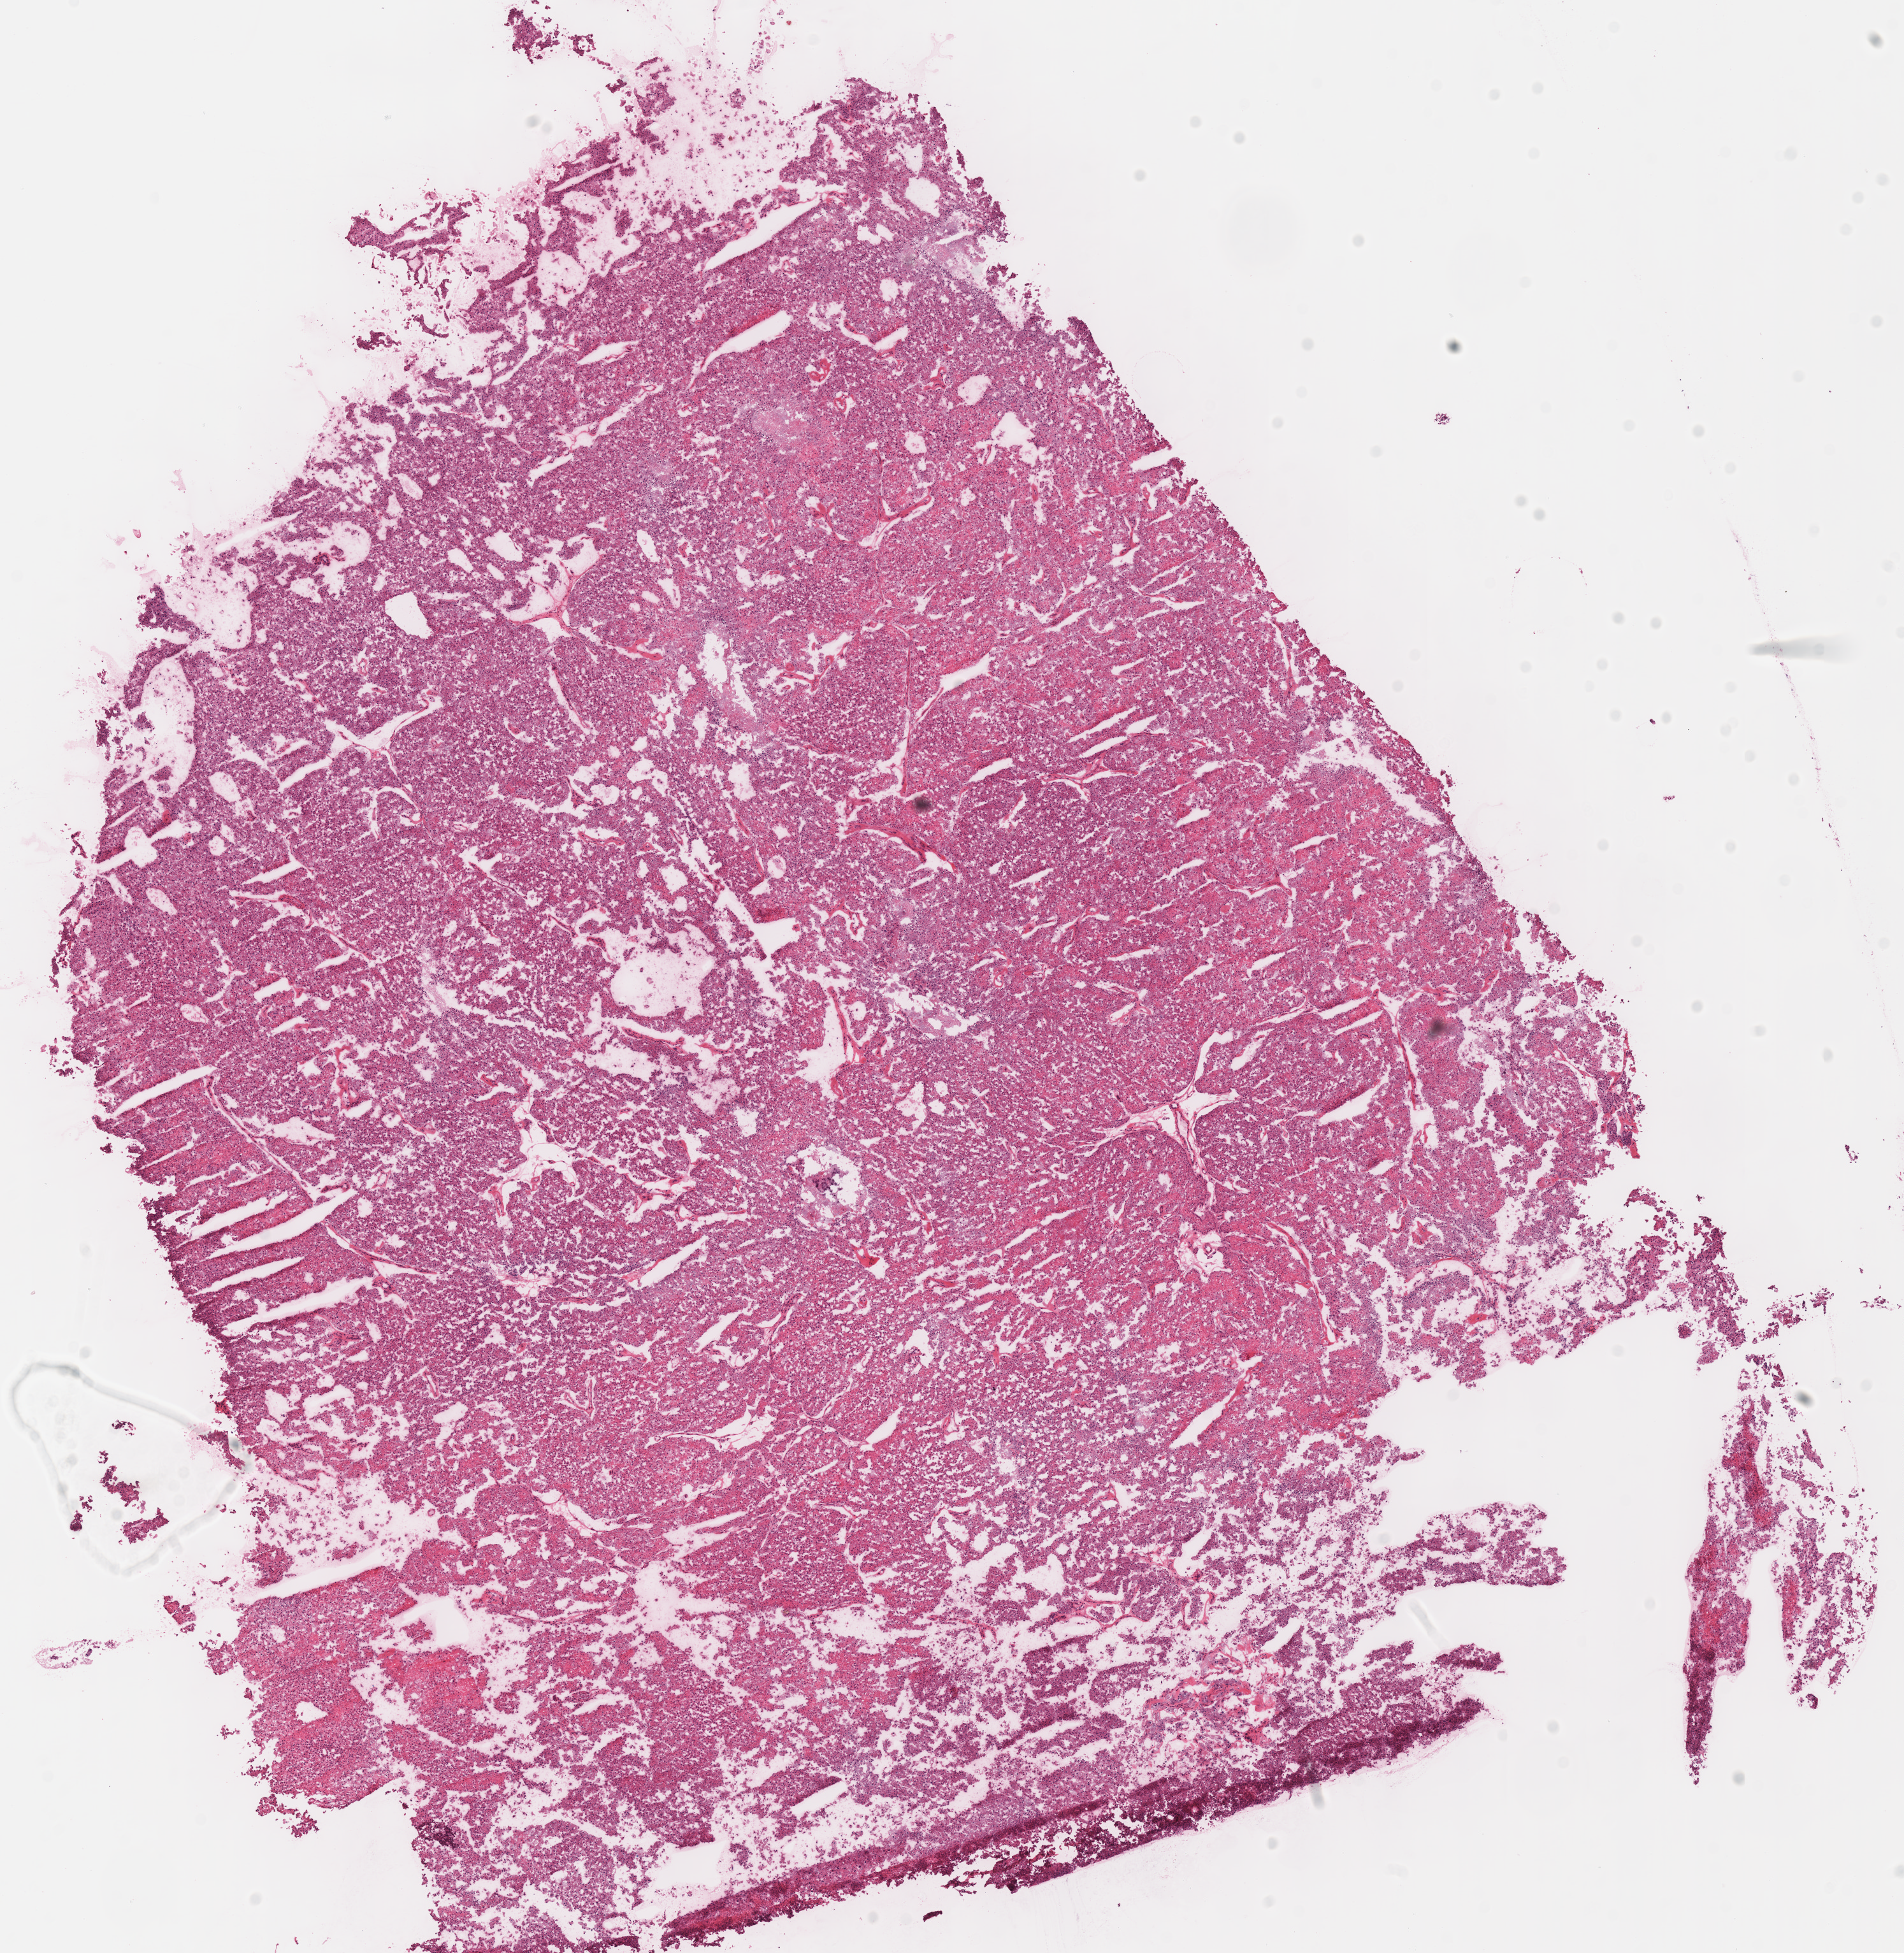
Whole-slide histology image, Hematoxylin and eosin (H&E) stained — low-resolution overview of the scanned area, about 11.7 x 12.0 mm; frozen section from the top of the tissue portion; kidney, primary tumour sample. Male patient; age at initial diagnosis 62 years. Composition of this section per pathologist review: tumour cells 95%, tumour nuclei 95%, normal cells 0%, stromal cells 5%, necrosis 0%.
• diagnosis: Renal cell carcinoma, chromophobe type
• lymph nodes positive (case pathology): 0 of 1 examined
• AJCC pathologic stage: II